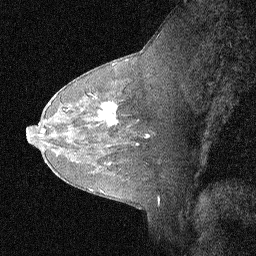
Breast MRI (dynamic contrast-enhanced), one sagittal slice; slice 41 of 64 in the series (ordered by position); dynamic contrast-enhanced study with each time point stored as its own series, time point 2 of 3 at this slice position (early post-contrast, ordered by acquisition time); 1.5 T; TE 4.5 ms, TR 11 ms; 256 × 256 image matrix. Female patient, age 62 years. From the clinical record (not read from this slice): setting: breast cancer imaged before/during neoadjuvant chemotherapy; receptor status: HR-positive, HER2-negative.
Outlined on this slice (semi-automatically segmented with operator editing):
- analysis volume of interest (the breast-tissue region the enhancement analysis was run in; not a lesion): box from (x=91, y=93) to (x=124, y=129) px
- tumour enhancement mask (voxels above the 90 % enhancement threshold inside the analysis volume of interest): (x=91, y=94)–(x=121, y=126)